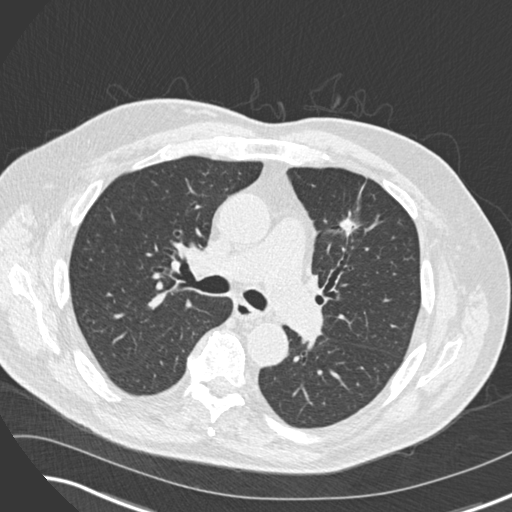
Low-dose screening chest CT, axial slice; third screening round (two years after baseline); lung window (W 1500 / L -600 HU); standard (soft-tissue) reconstruction kernel (B30f); 512 × 512 image matrix, field of view 360 × 360 mm. Male participant, aged 74 years at enrolment. Former smoker at enrolment.
- Lesion marked by an expert reader, bounding box <320,199,377,249> (left, top, right, bottom; pixels).
- The exam's reader record, not a measurement of the box and not confirmed to be the same lesion: non-calcified nodule or mass ≥4 mm, left upper lobe, 12 × 10 mm, spiculated (stellate) margins, soft tissue attenuation, pre-existing on the prior screen: yes; interval growth: yes.
- Lung cancer was diagnosed 349 days after this screen: adenocarcinoma, NOS, left upper lobe, poorly differentiated (G3), stage IIIA (AJCC 6th edition), 27 mm at pathology.